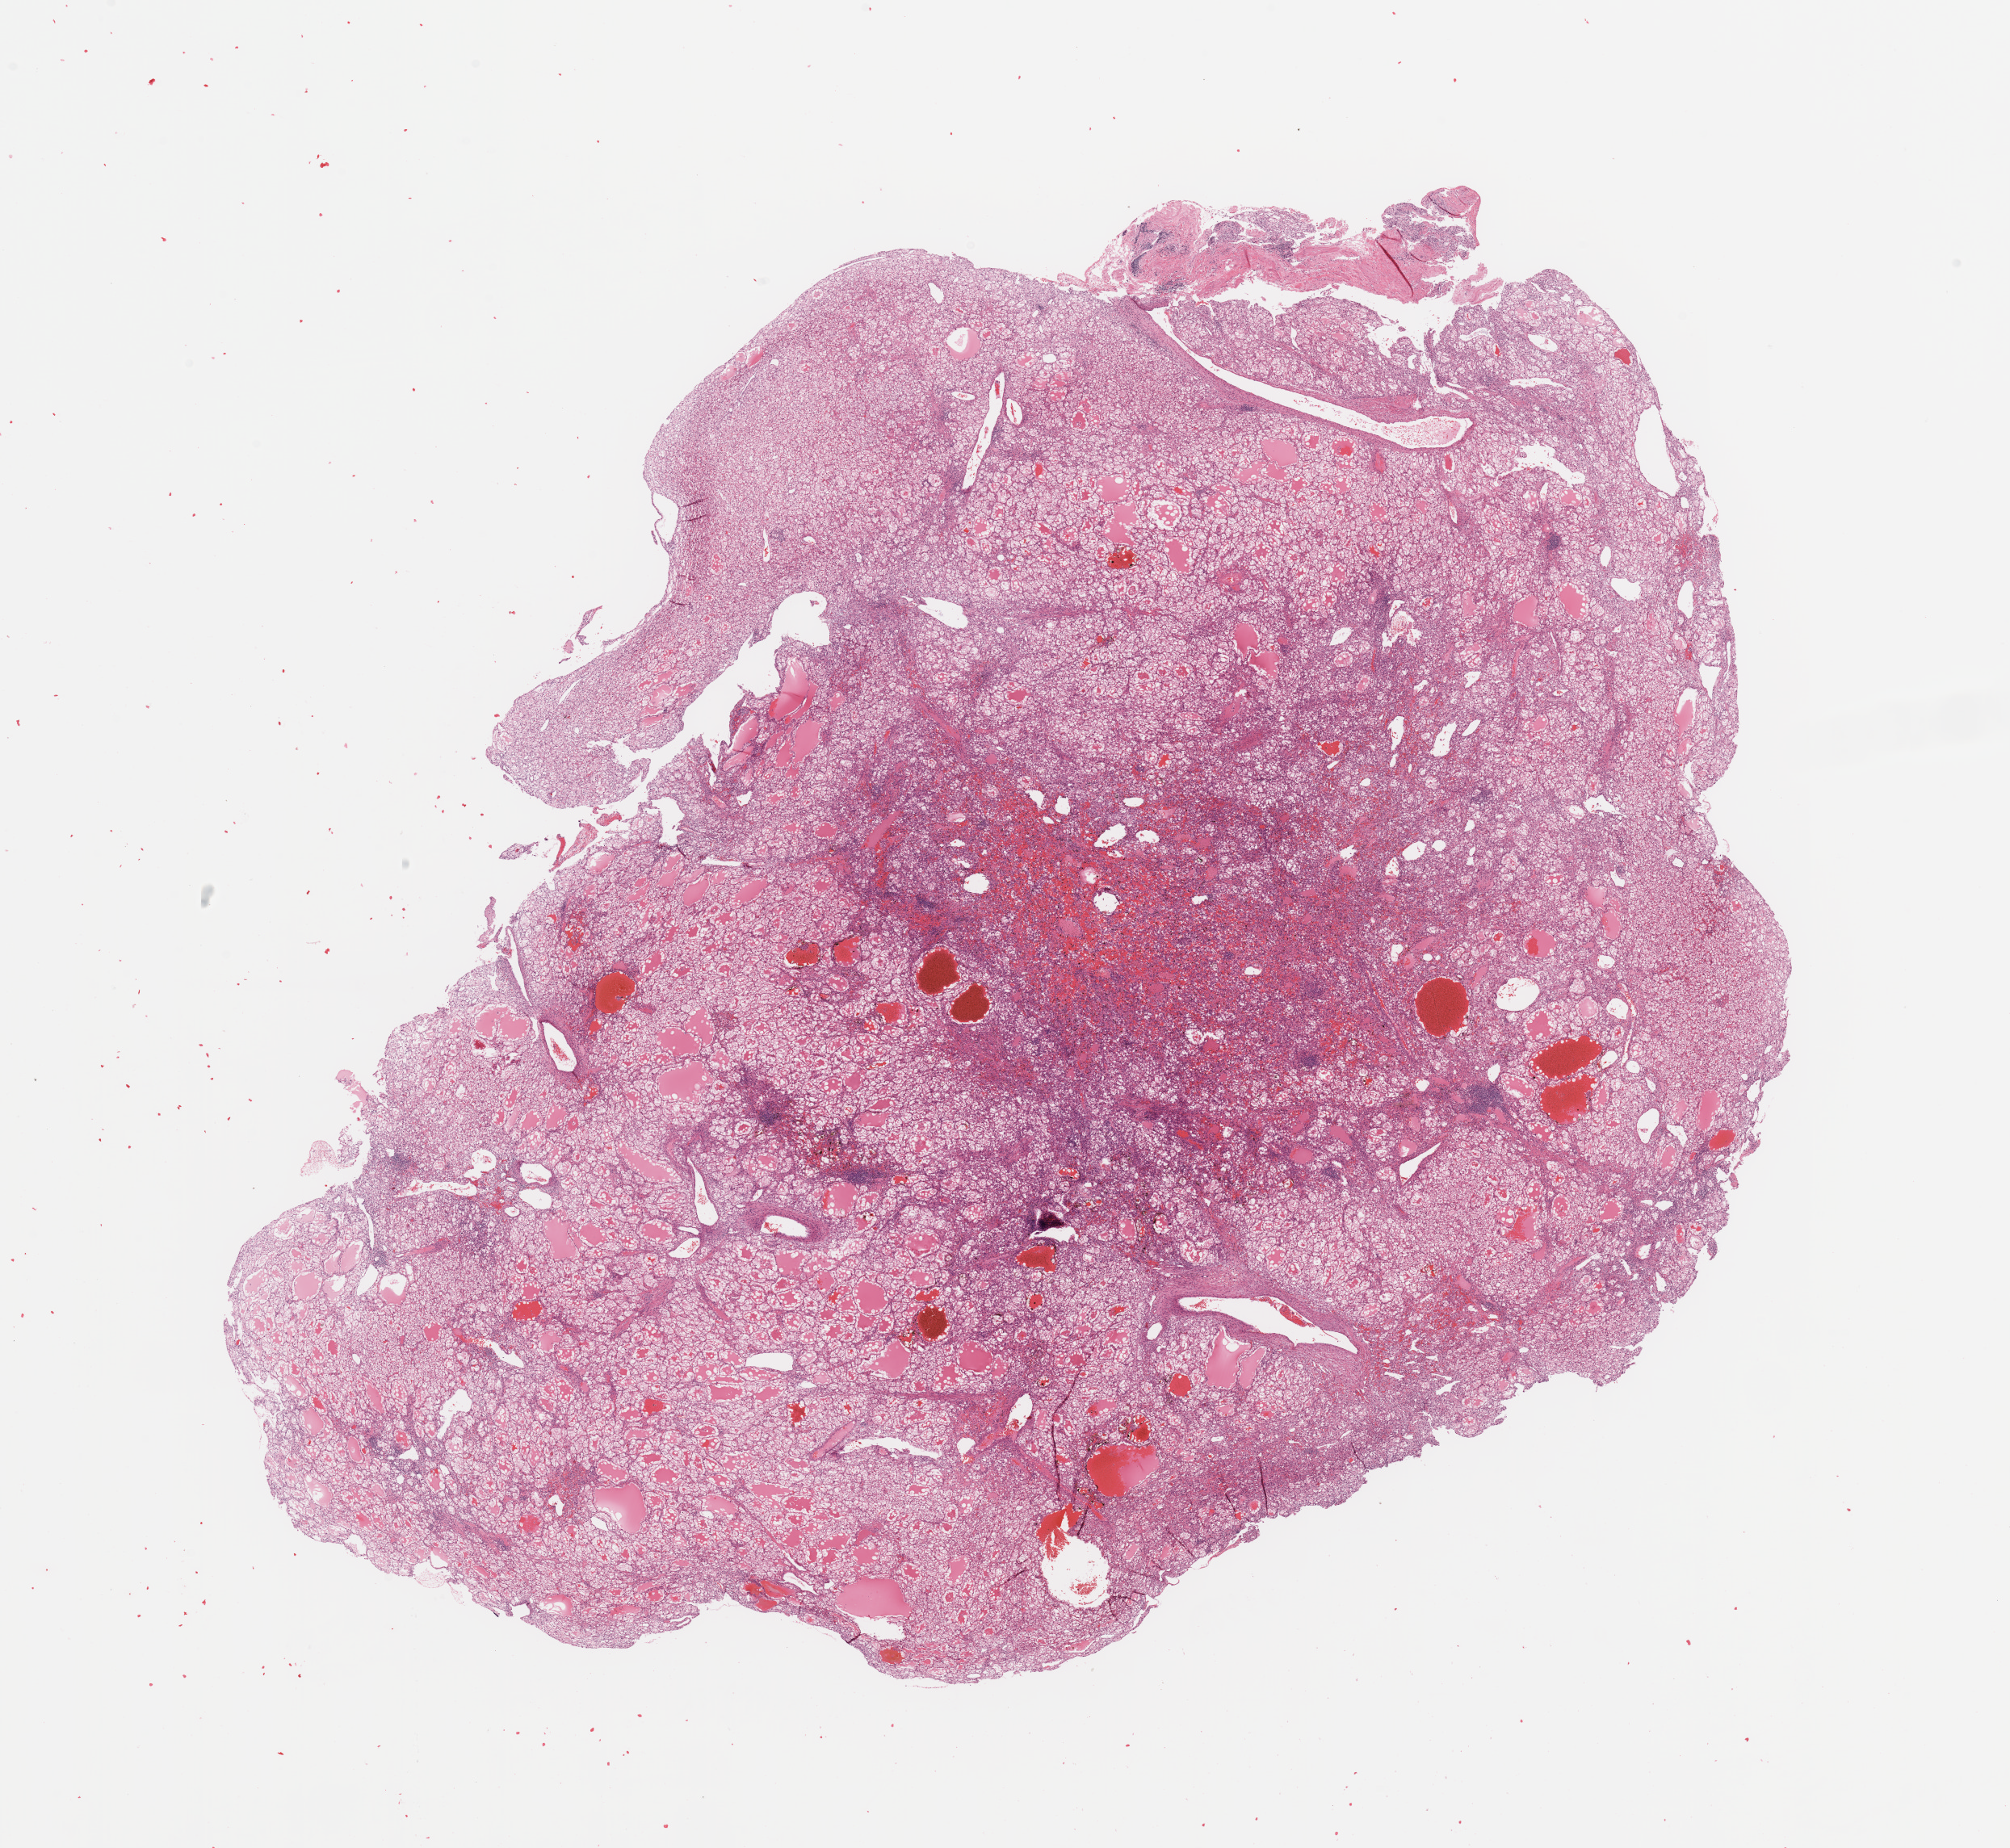
H&E whole-slide image — shown as a low-resolution overview of the whole scanned area (about 19.7 x 18.1 mm, acquisition: 20x scan). Kidney, tumour tissue. 42-year-old female patient.
Histologic diagnosis: Renal cell carcinoma, NOS.